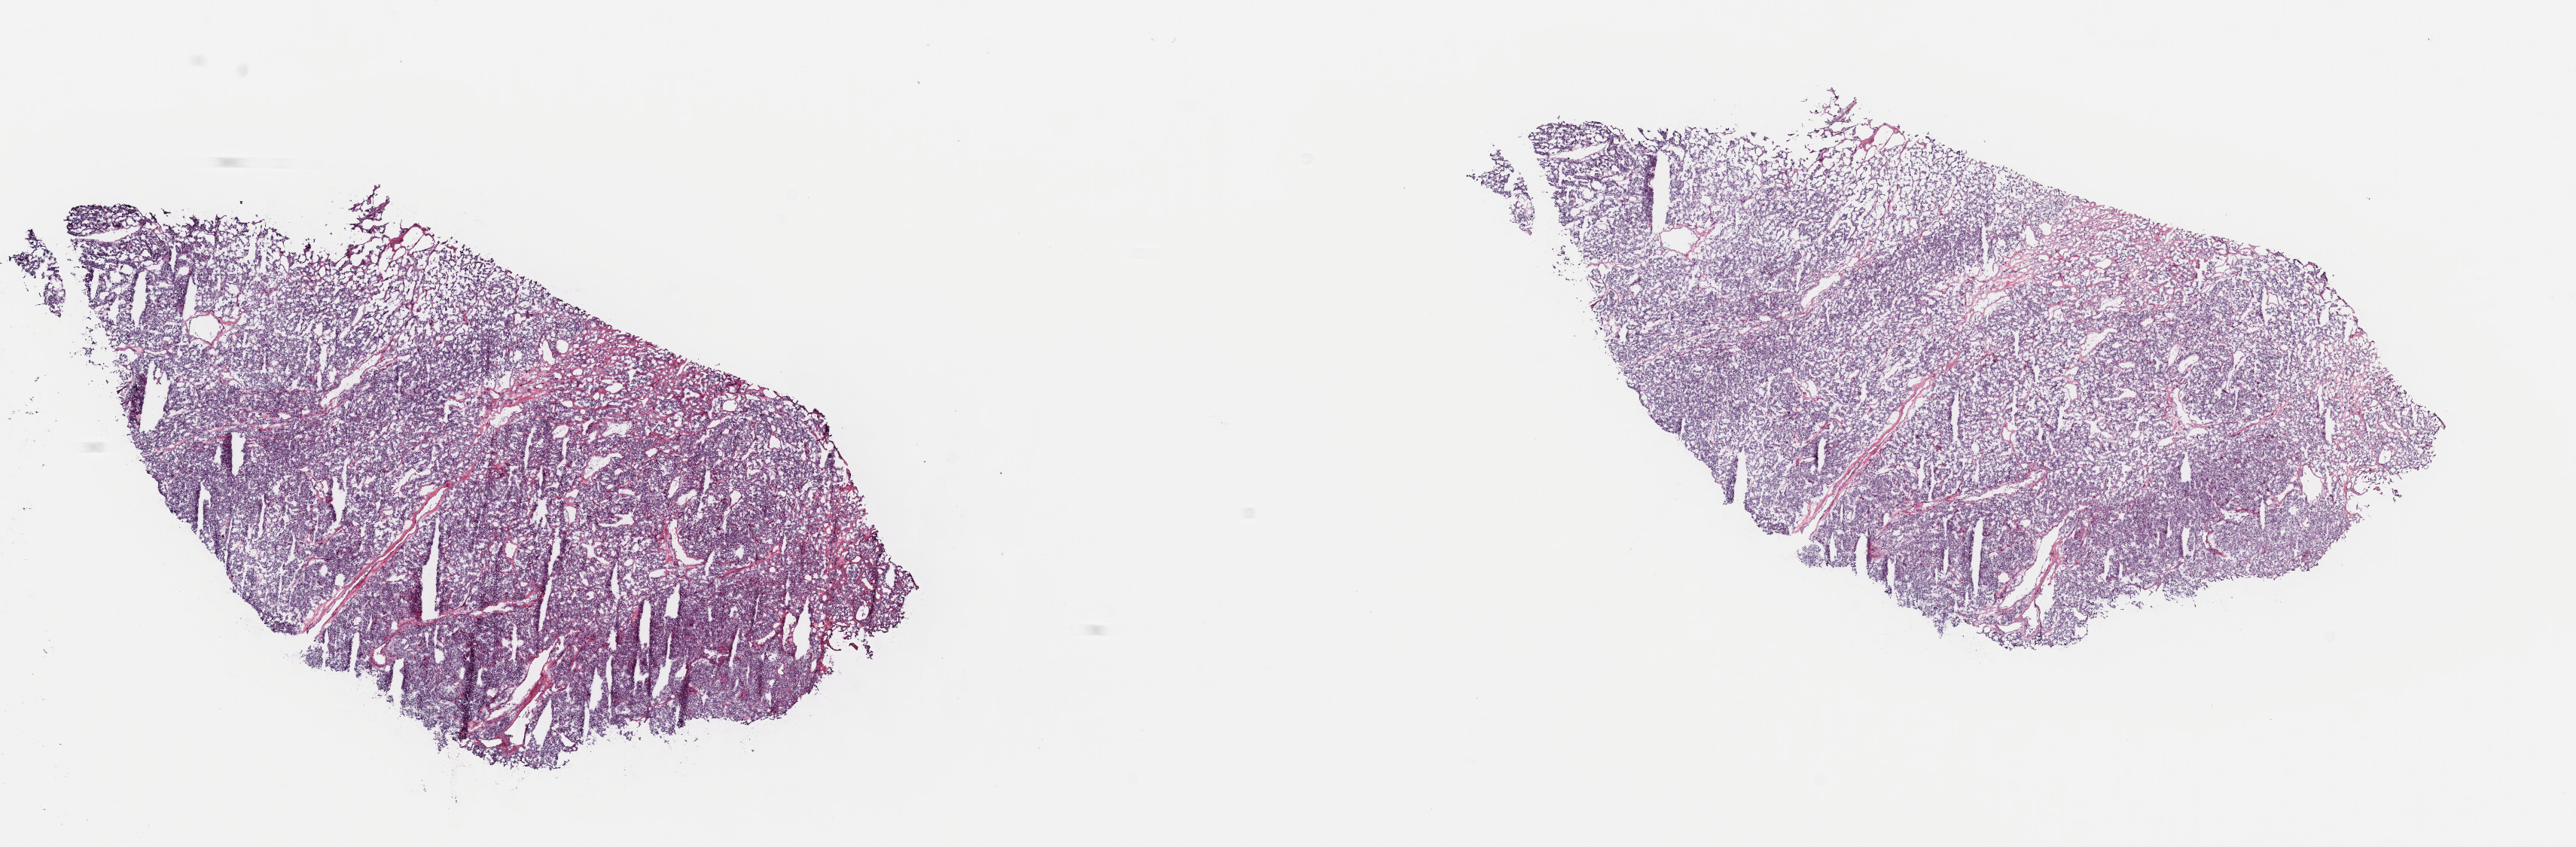
Whole-slide histology image, H&E, whole scanned area (about 27.0 x 8.9 mm) shown as a low-resolution overview, frozen section, connective, subcutaneous and other soft tissues, primary tumour sample. Patient: female, age at initial diagnosis 57 years. Composition of this section per pathologist review: tumour cells 100%, tumour nuclei 80%, normal cells 0%, stromal cells 0%, necrosis 0%. Infiltration values recorded for this section: lymphocyte infiltration 1%, monocyte infiltration 0%, neutrophil infiltration 0%.
* histologic diagnosis: Paraganglioma, NOS (connective, subcutaneous and other soft tissues of abdomen)